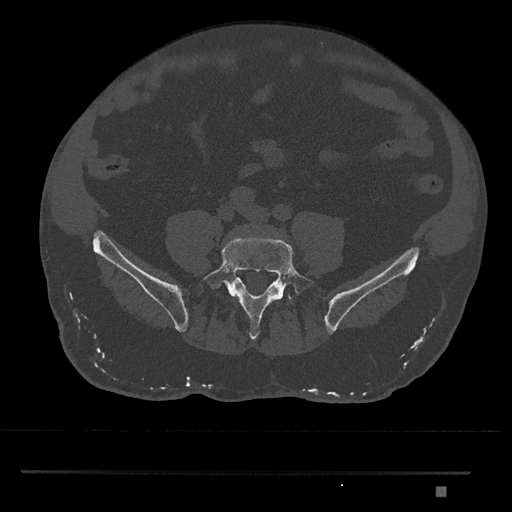
CT including the spine, one axial slice. Slice 560 of 1134 in the series (ordered by position). Reconstruction kernel Br40s/3. Bone window (W 1800 / L 400 HU). 512 × 512 image matrix, field of view 429 × 429 mm. Male patient, age 65 years. From the clinical record (not read from this slice): primary cancer: prostate.
Annotated regions visible in this slice (semi-automatically segmented with operator editing):
- L5 vertebra: bounding box <203,237,317,340> (left, top, right, bottom; pixels)